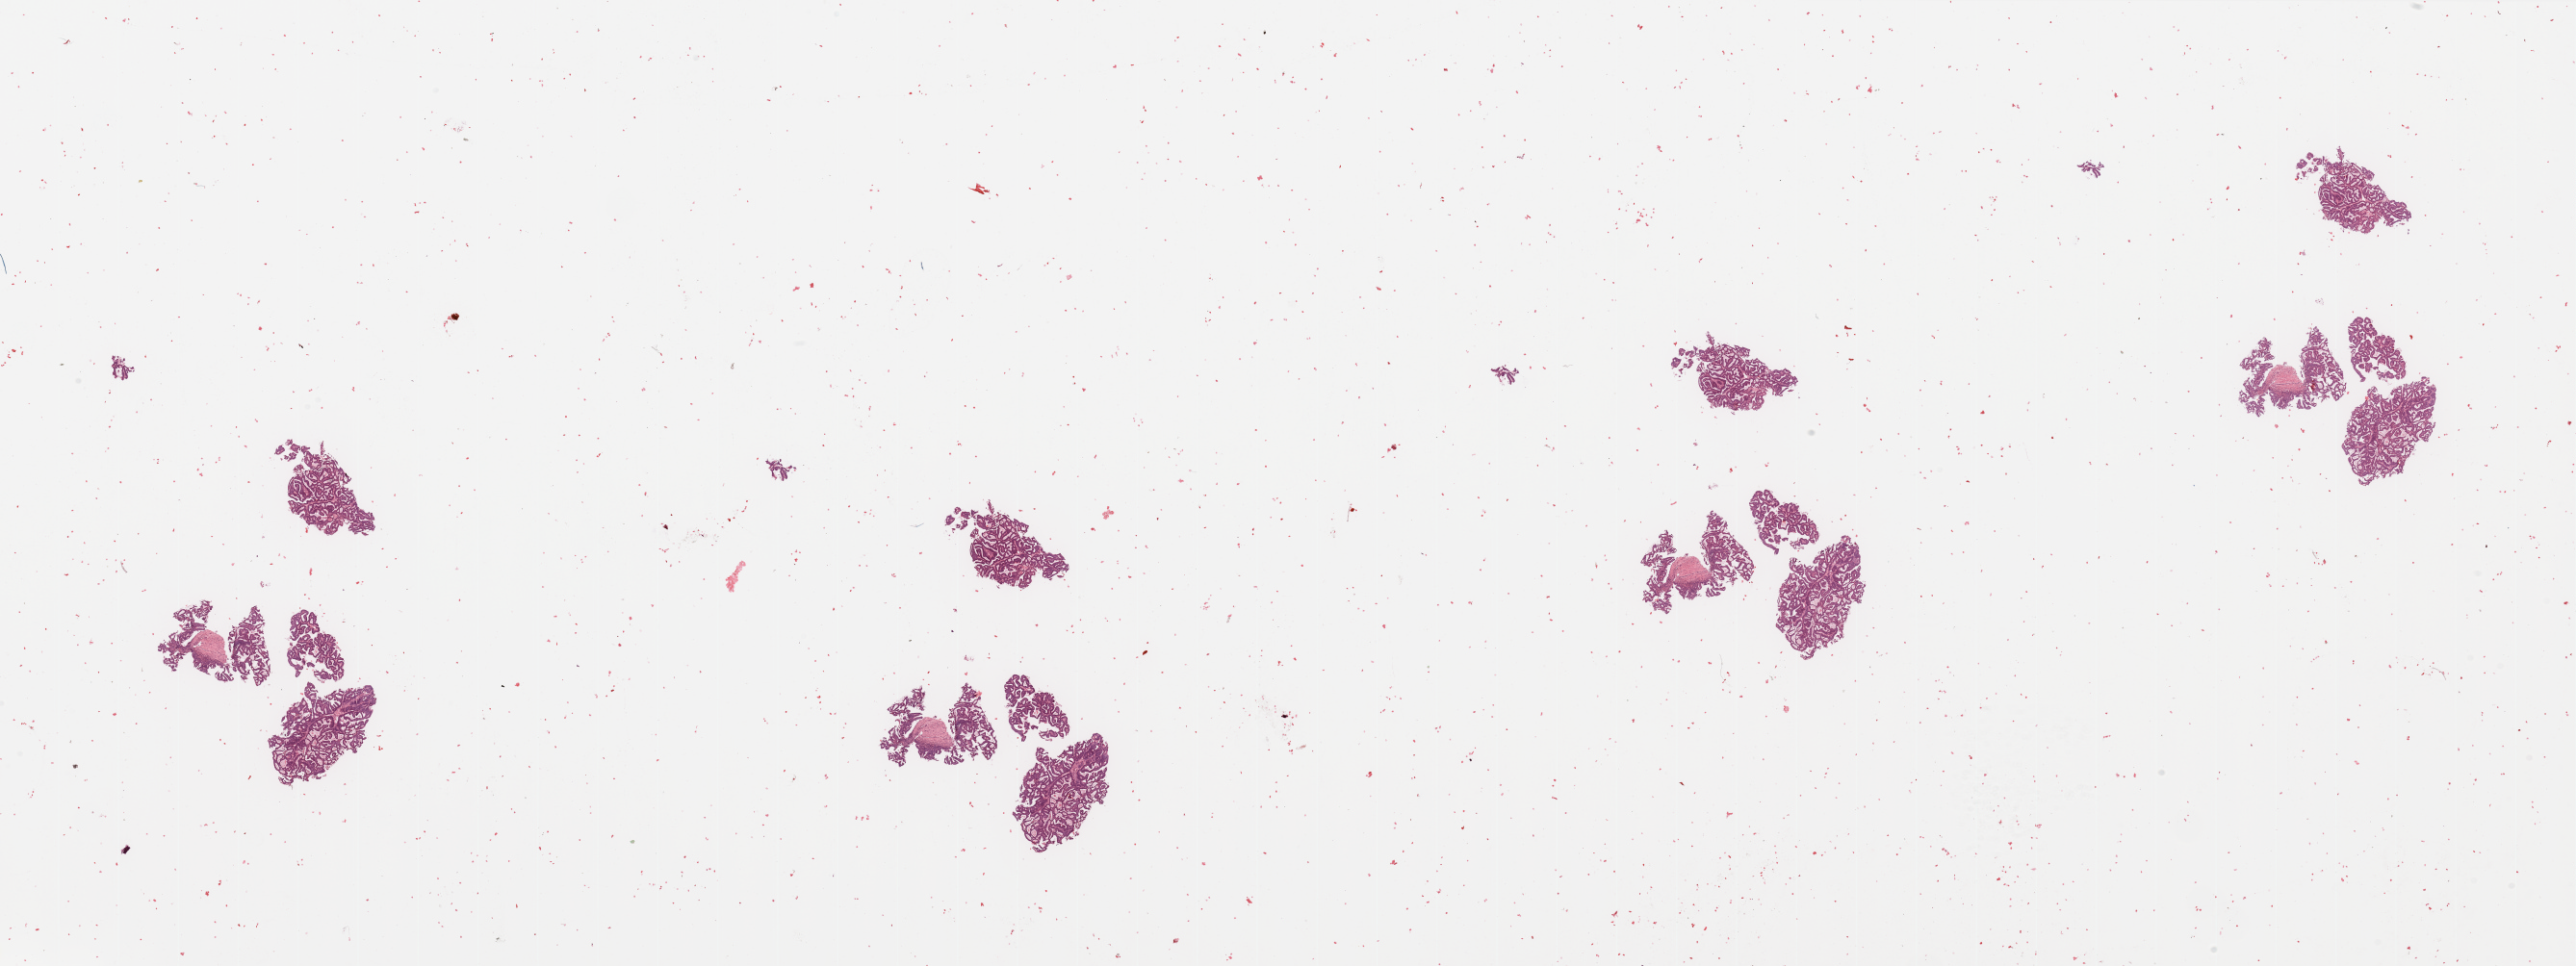
H&E whole-slide image, a low-resolution overview of the entire scanned area, about 42.3 x 15.9 mm, tumour tissue sample, uterus. Female, 65 y/o. Histologic grade: G2 (moderately differentiated).
* primary tumour site (as recorded): anterior endometrium
* AJCC pathologic stage: I
* diagnosis: Endometrioid adenocarcinoma, NOS